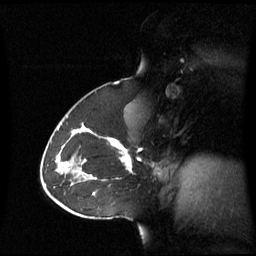
Breast MRI (dynamic contrast-enhanced), one sagittal slice. Dynamic contrast-enhanced series, image 2 of 3 at this slice position (ordered by acquisition). 1.5 T. TE 4.2 ms, TR 8.4 ms. 2.8 mm slice thickness. 256 × 256 image matrix, field of view 270 × 270 mm. Patient: female, 43 years. Case-level facts recorded for this patient, not image findings: setting: breast cancer imaged before/during neoadjuvant chemotherapy; receptor status: triple-negative.
Outlined on this slice (semi-automatic segmentation, software-assisted and operator-edited):
- analysis volume of interest (the breast-tissue region the enhancement analysis was run in; not a lesion): bounding box <62,124,134,180> (left, top, right, bottom; pixels)
- tumour enhancement mask (voxels above the 70 % enhancement threshold inside the analysis volume of interest): <105,137,132,171>